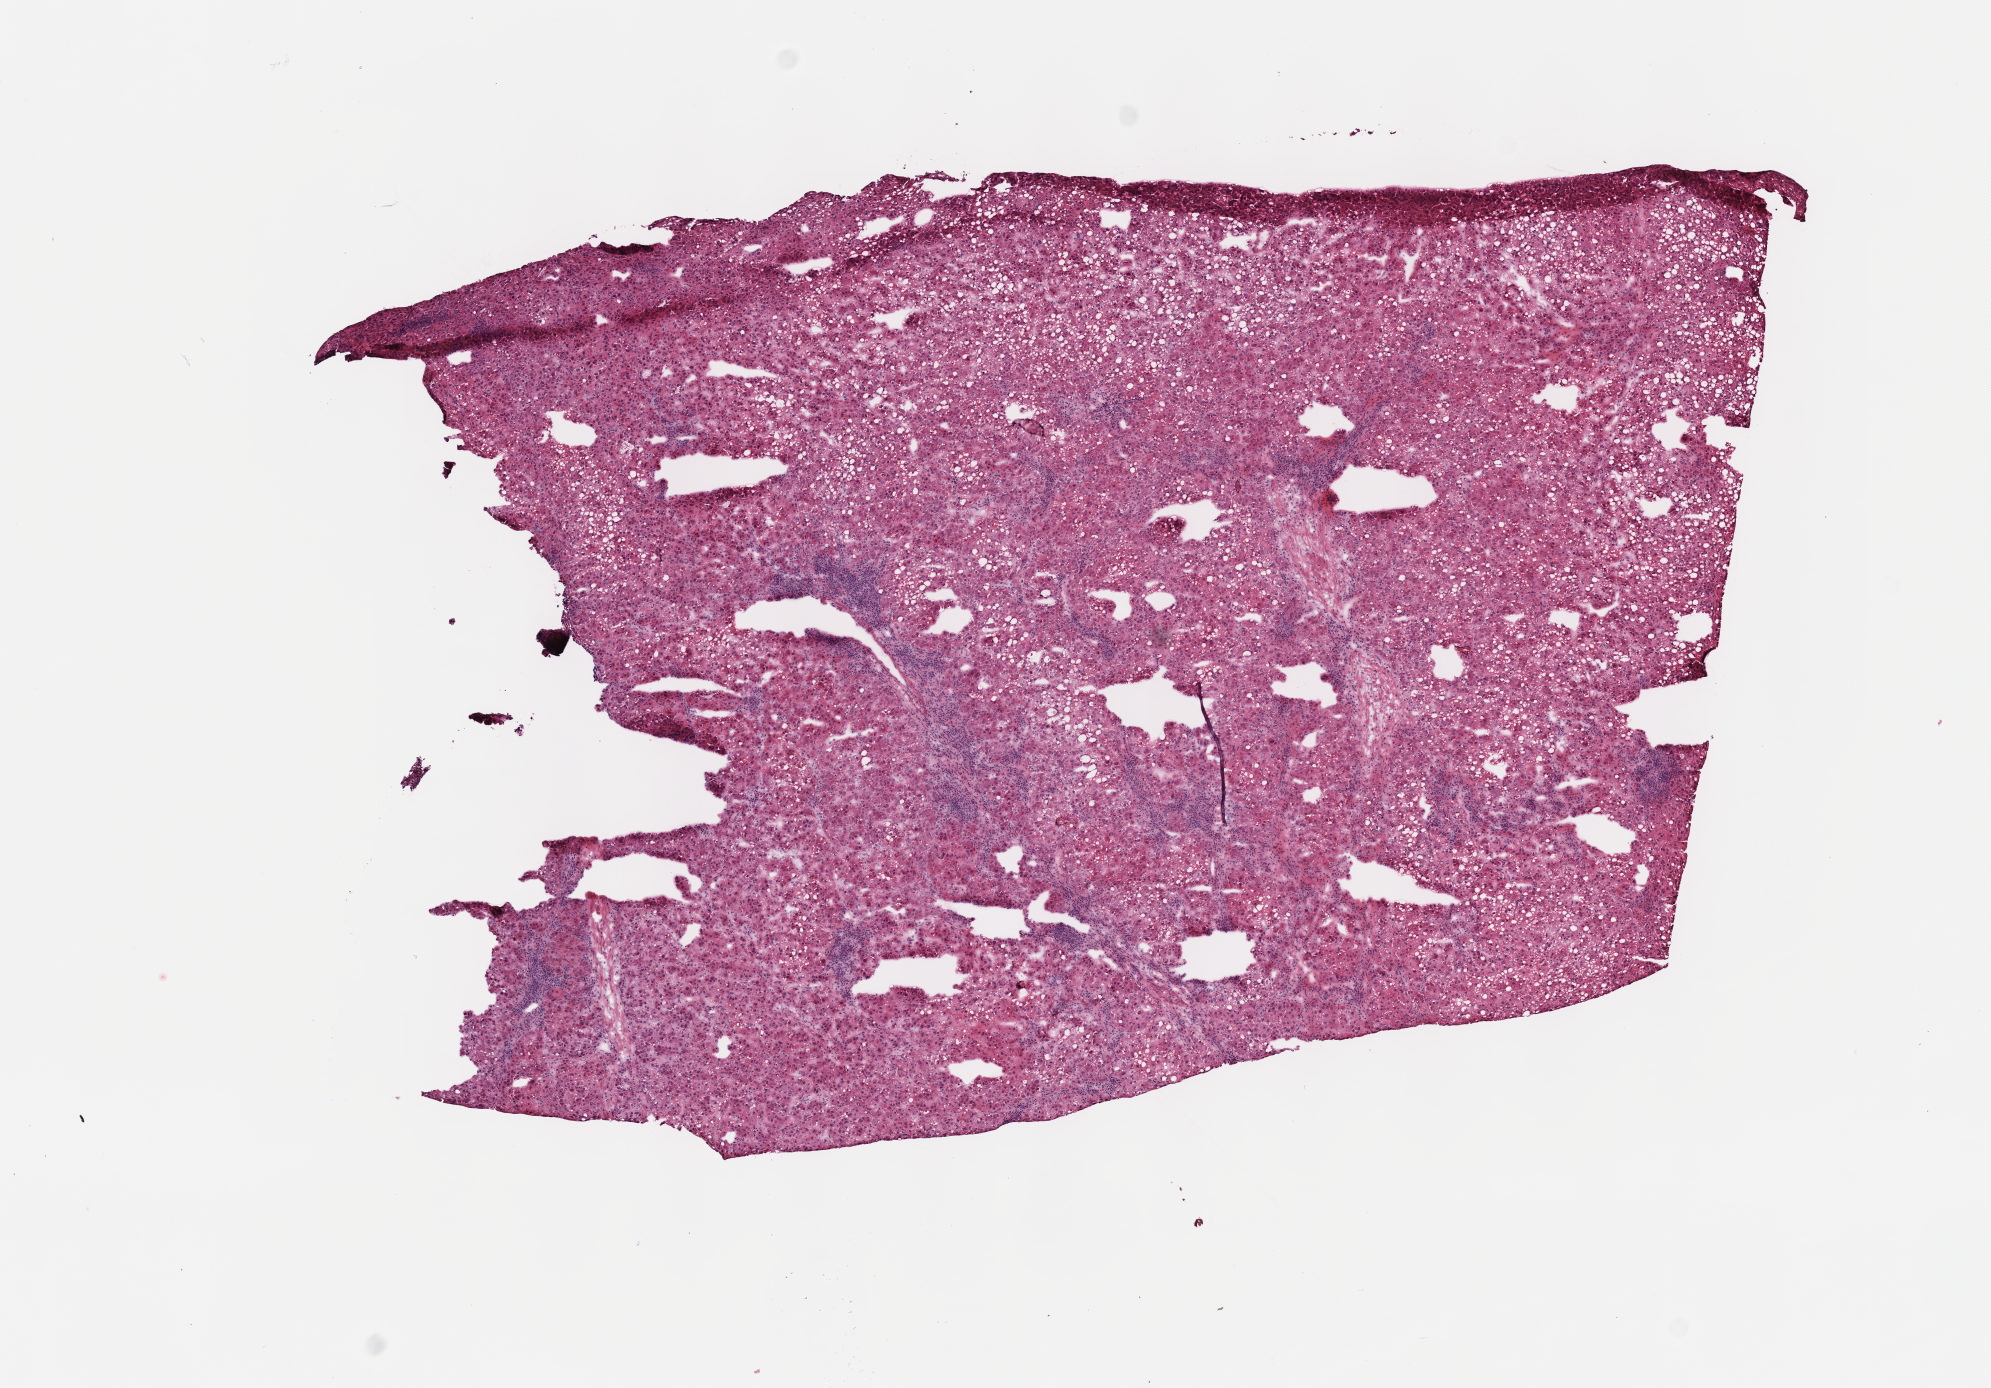
Whole-slide histology image, Hematoxylin and eosin (H&E) stained — a low-resolution overview of the entire scanned area, about 8.1 x 5.6 mm (slide scanned at 40x); frozen section from the top of the tissue portion; liver, primary tumour sample. Male patient; age at initial diagnosis 51 years. Histologic grade: G3 (poorly differentiated). Composition of this section per pathologist review: tumour cells 100%, tumour nuclei 75%, normal cells 0%, stromal cells 0%, necrosis 0%. Infiltration values recorded for this section: lymphocyte infiltration 7%, monocyte infiltration 0%, neutrophil infiltration 0%.
TNM: T2 N0 M0. AJCC pathologic stage: II (7th edition). Diagnosis: Hepatocellular carcinoma, NOS.